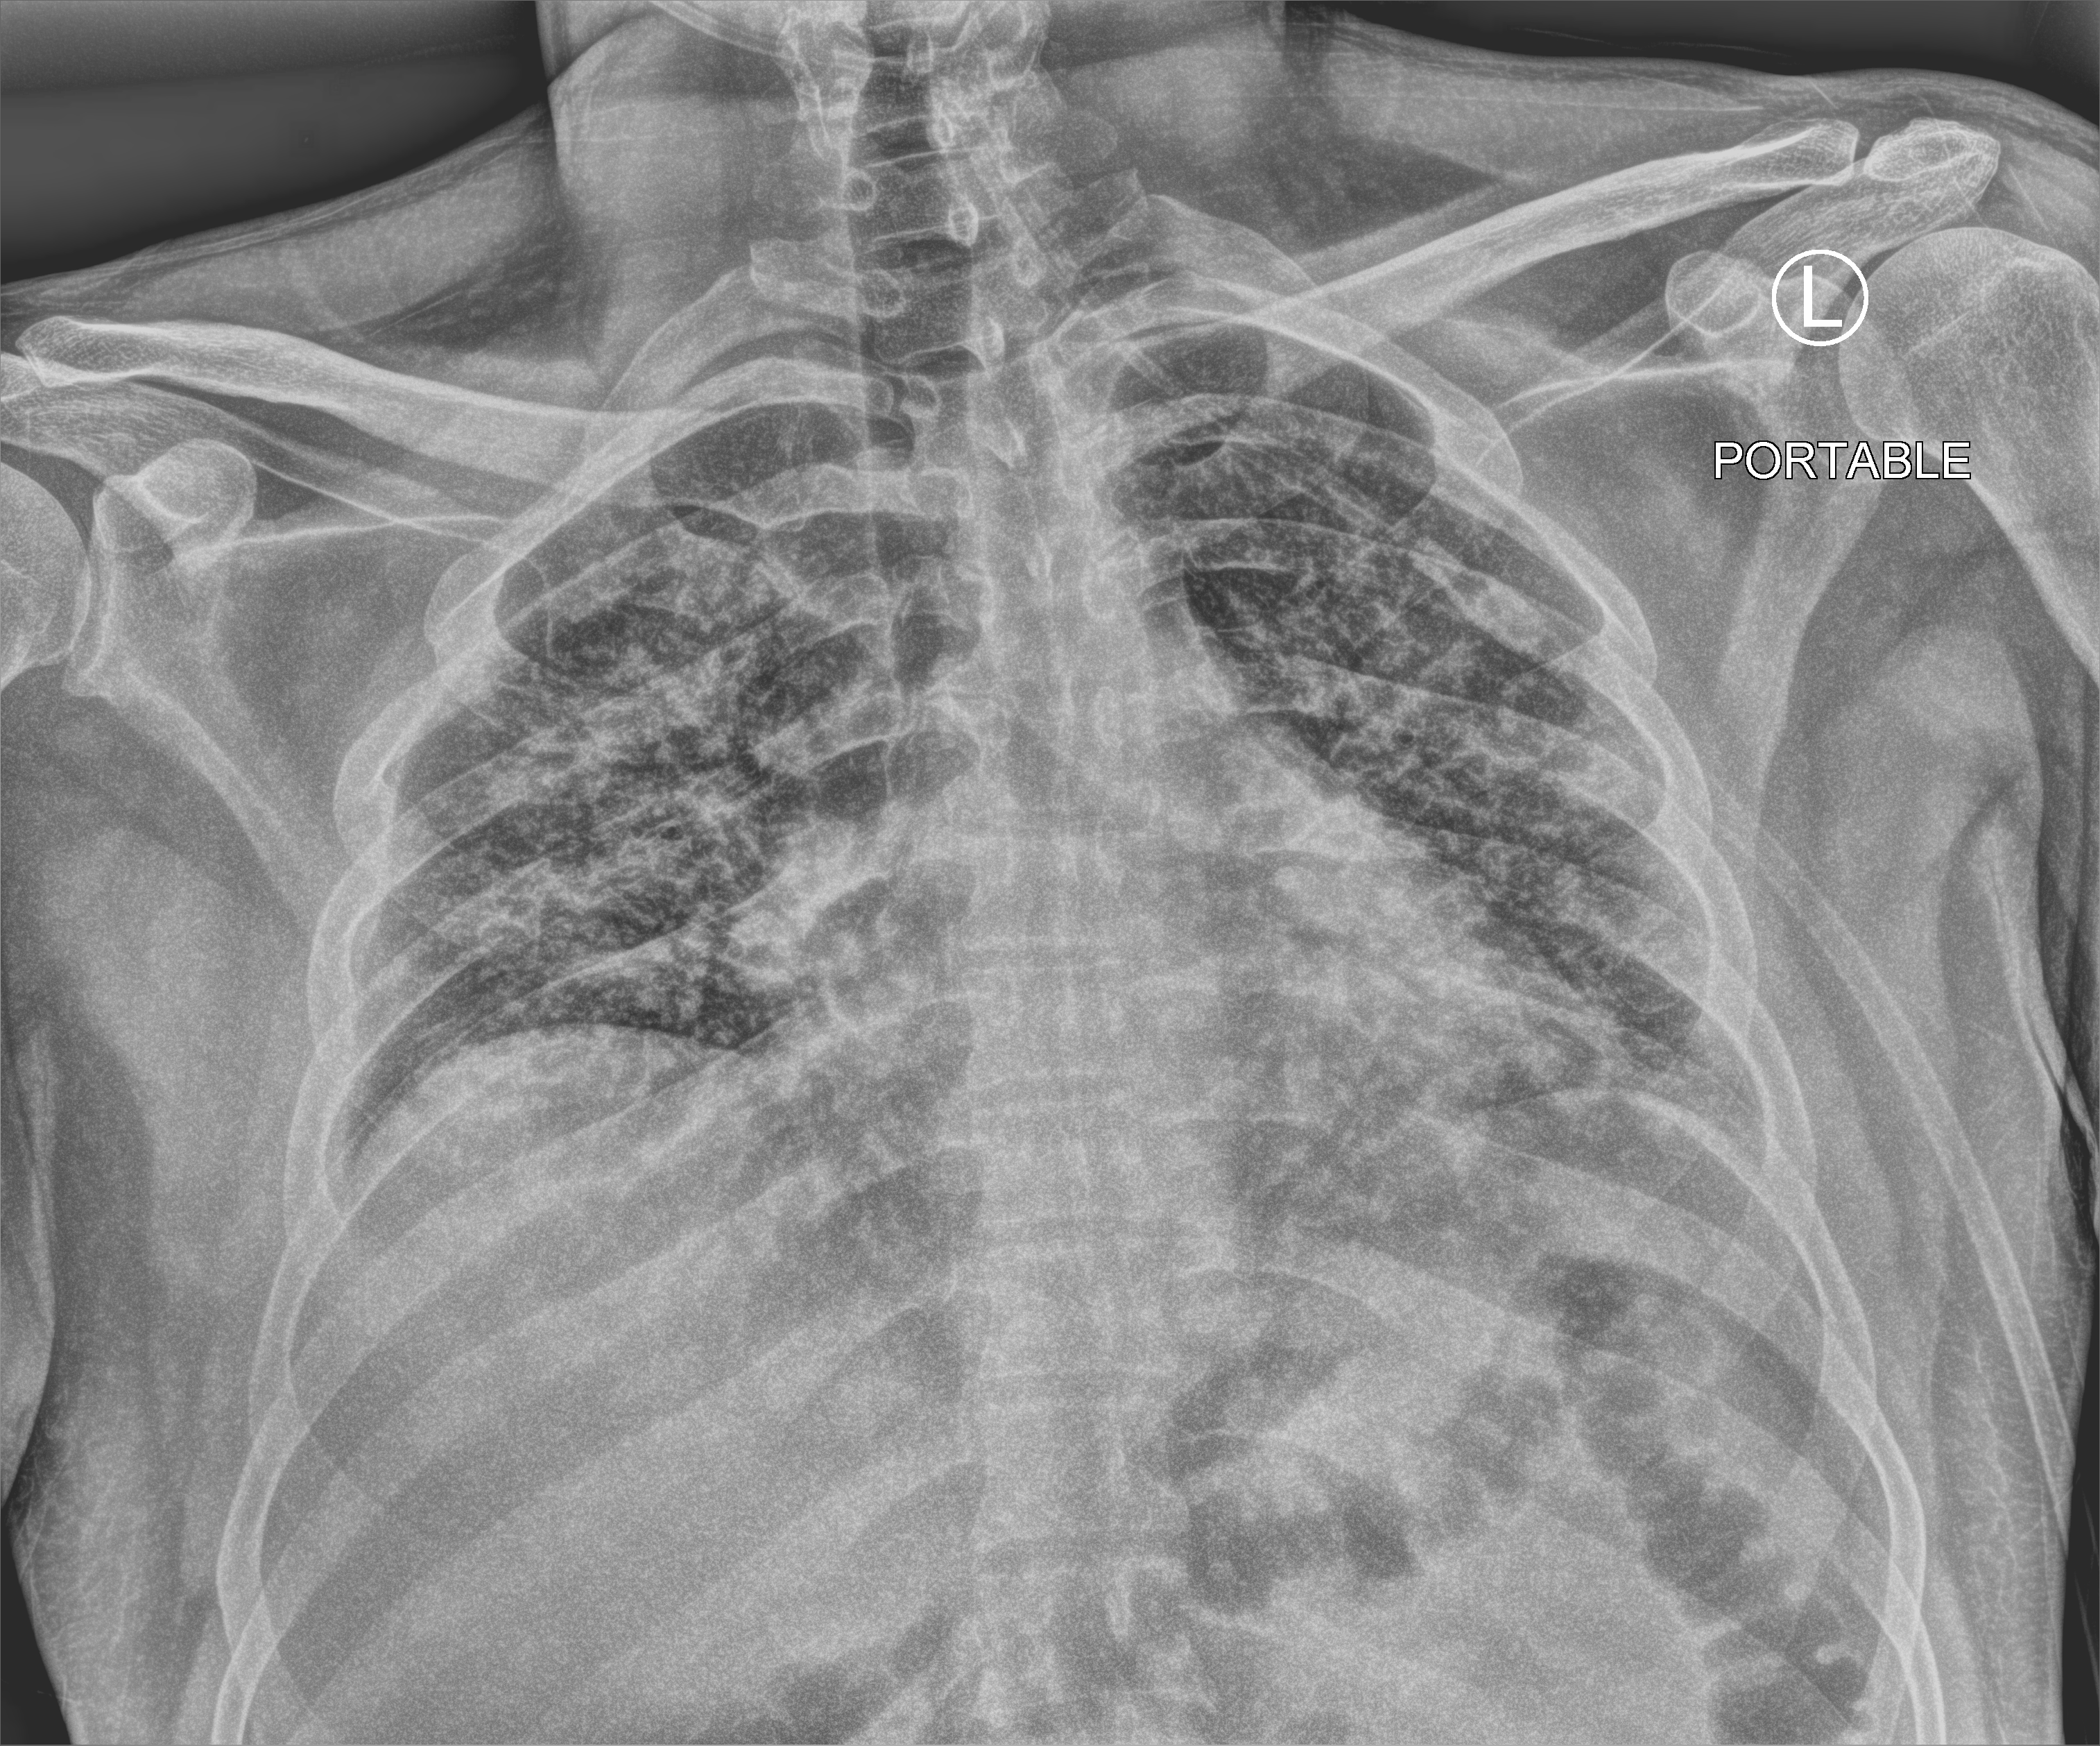
Chest X-ray (portable), anteroposterior (AP) projection. Patient hospitalised with COVID-19; male, aged 18–59 years.
From the hospital-stay record, not from the radiograph (when in the stay this image was taken is not recorded): mechanically ventilated during this hospital stay: no.